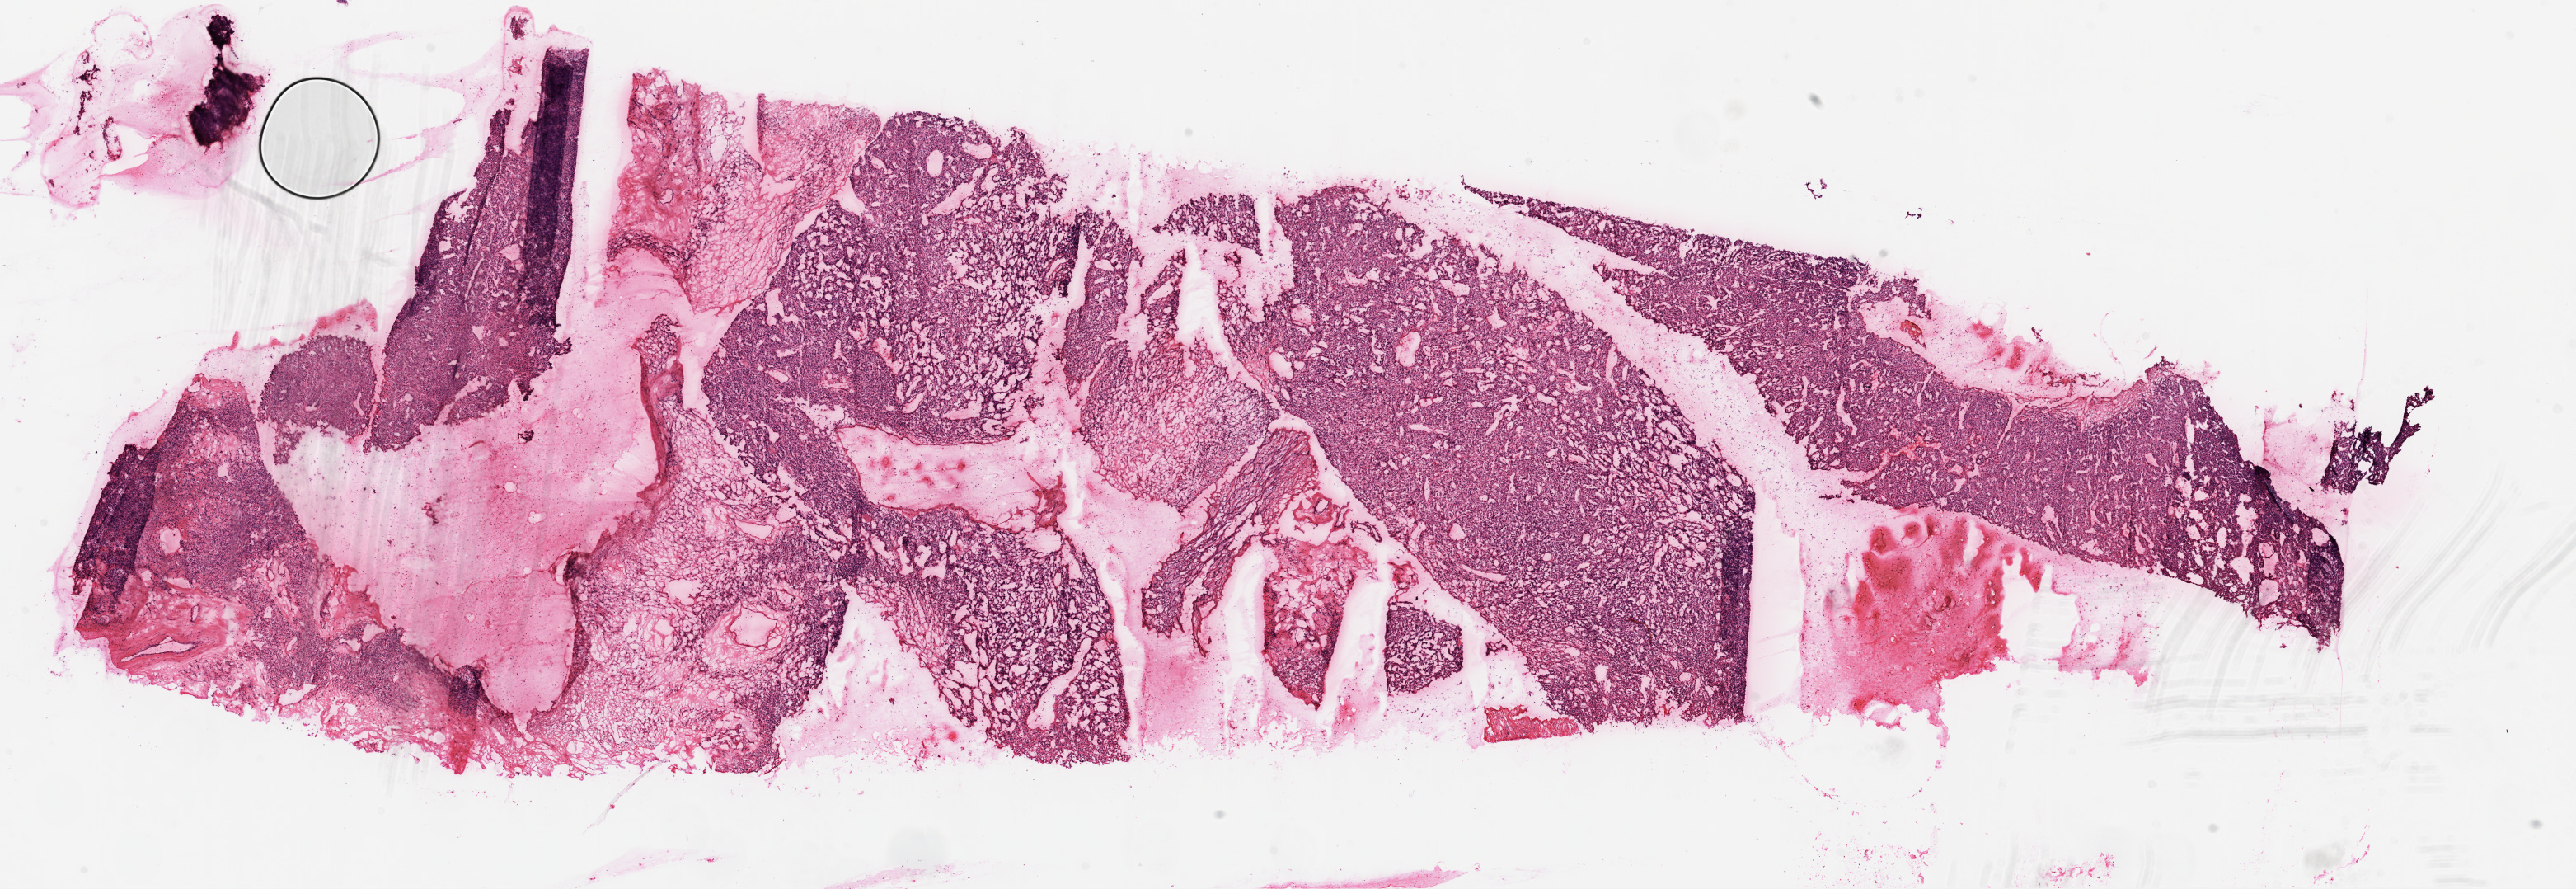
Whole-slide histology image, H&E-stained — a low-resolution overview of the entire scanned area, about 25.1 x 8.7 mm (acquisition: 20x scan), frozen section, primary tumour sample from the kidney. Patient: male, age at initial diagnosis 64 years. Histologic grade: G3 (poorly differentiated). Slide review estimates, as recorded: tumour cells 90%, tumour nuclei 85%, normal cells 0%, stromal cells 10%, necrosis 0%.
AJCC pathologic stage: IV (7th edition). Pathologic diagnosis: Clear cell adenocarcinoma, NOS.